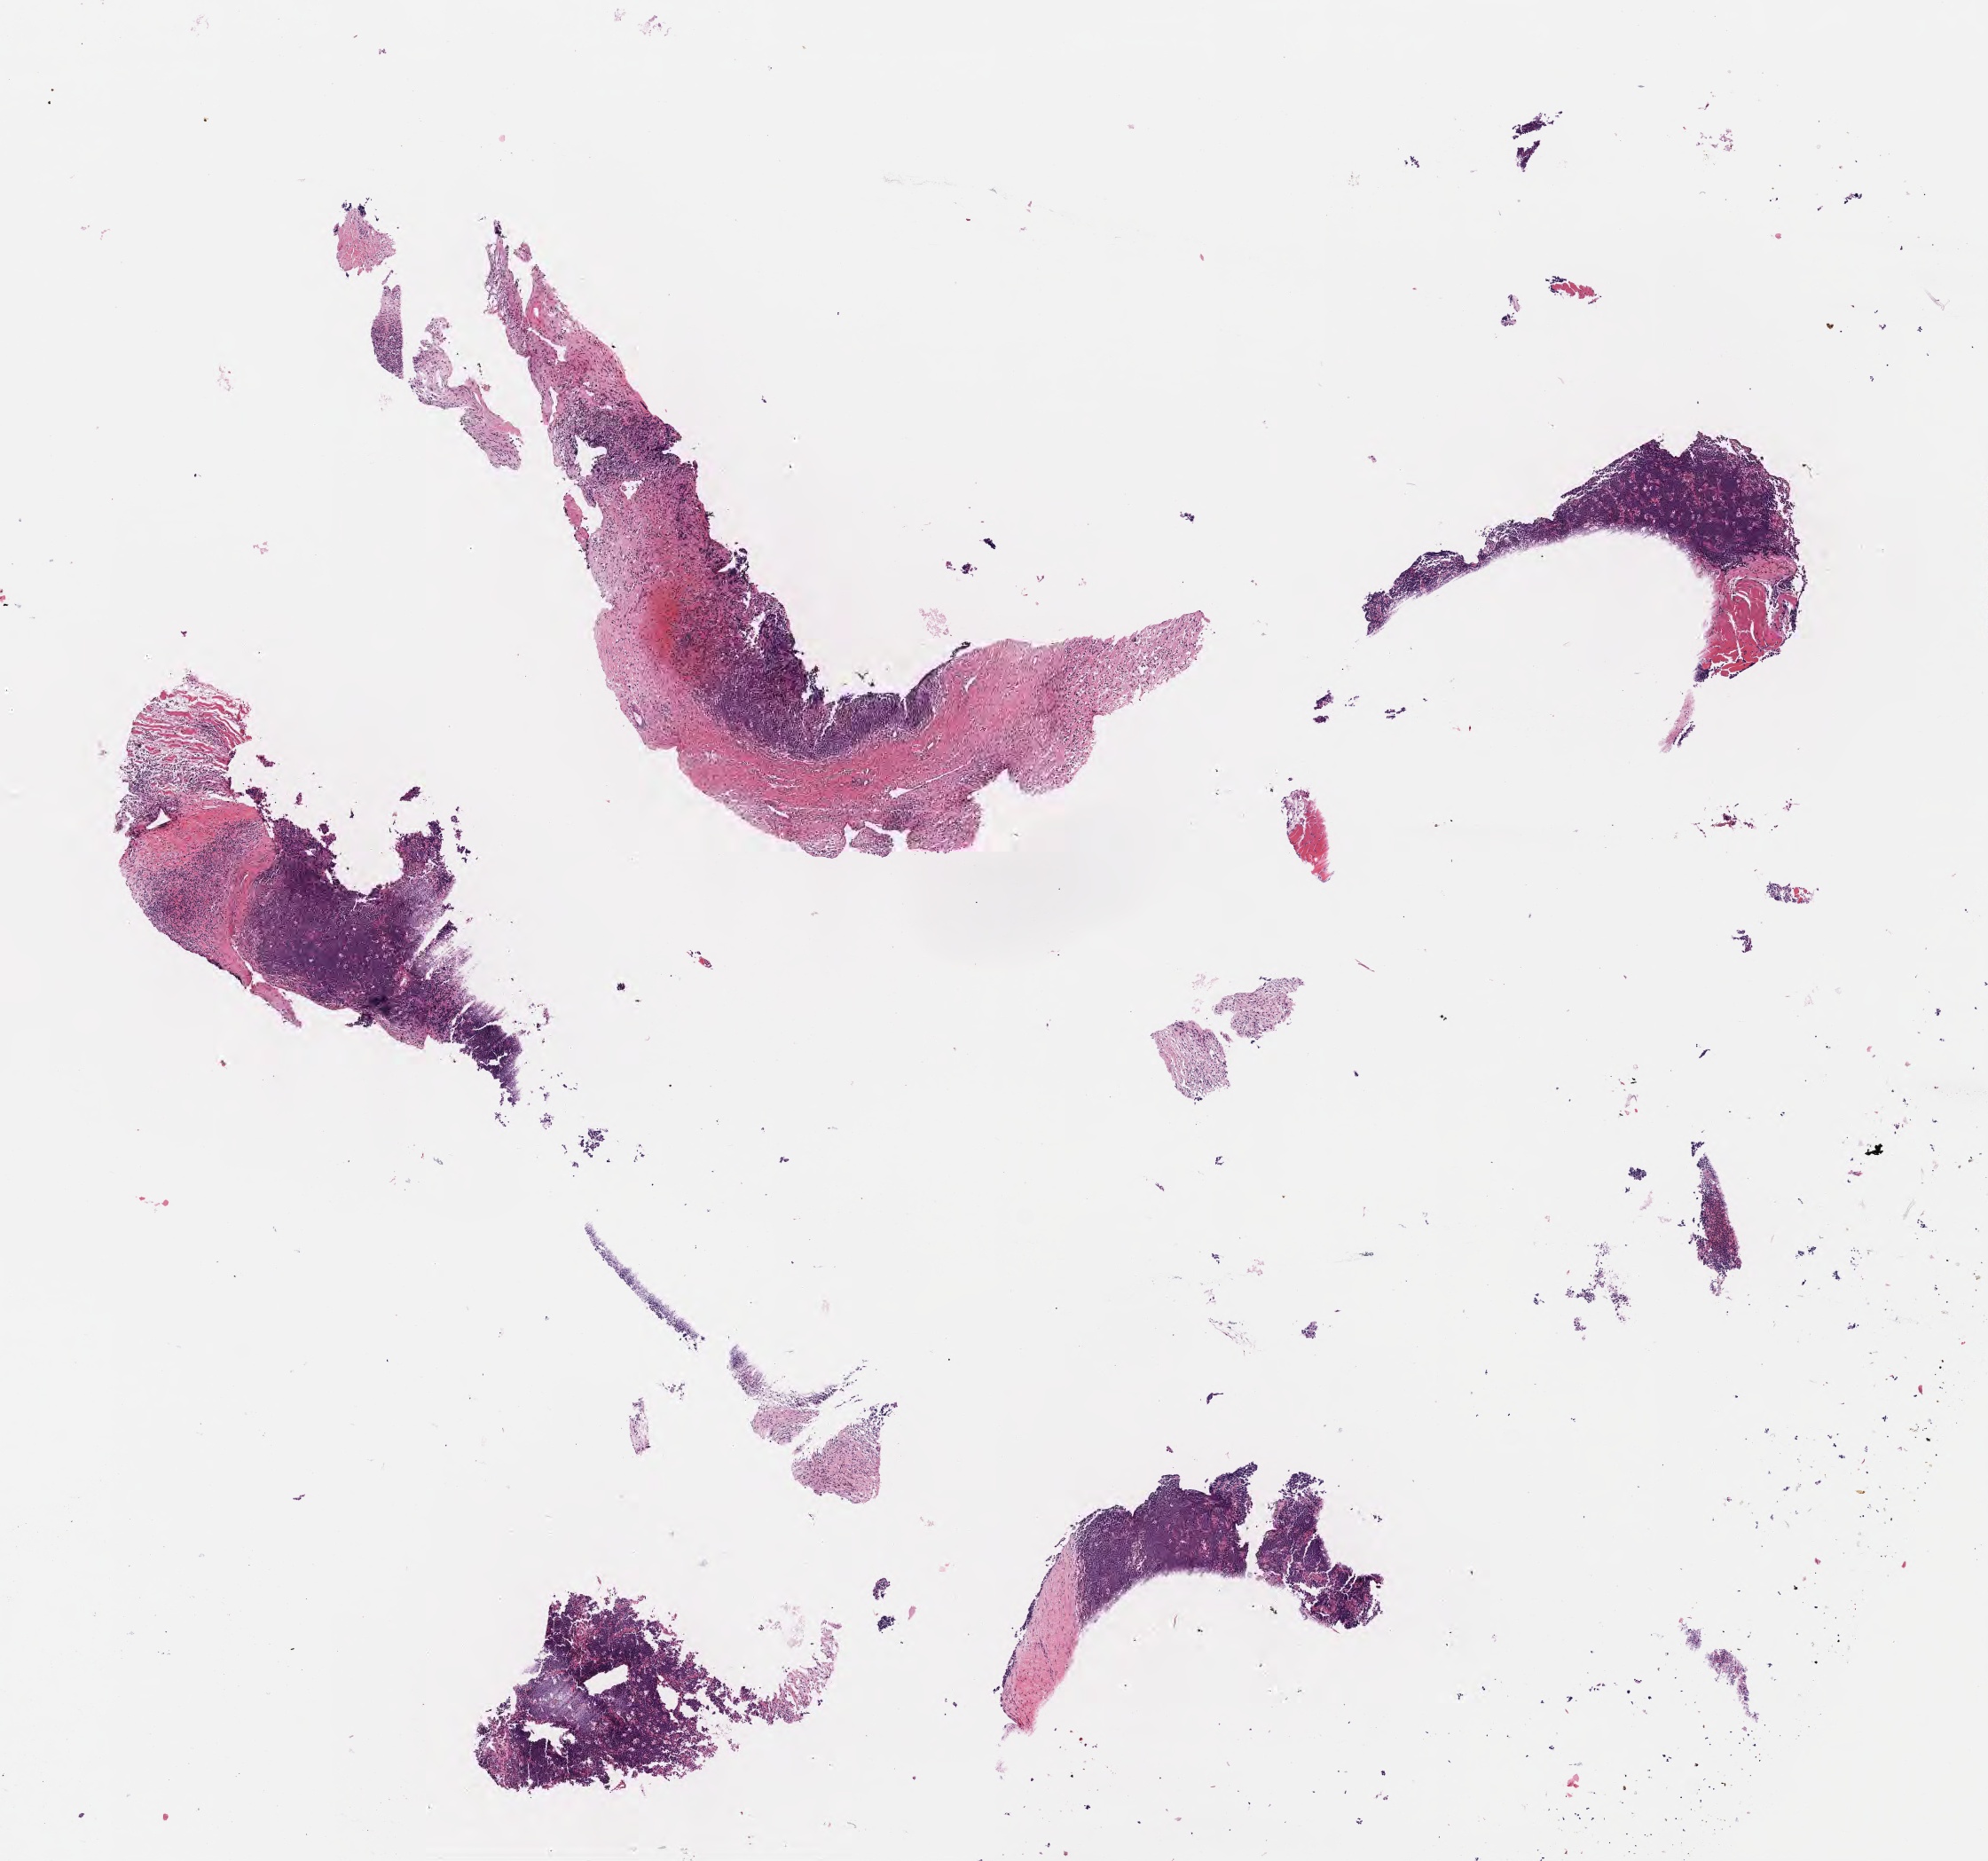
Whole-slide image, hematoxylin and eosin (H&E) stain, whole scanned area (about 9.1 x 8.5 mm) shown as a low-resolution overview. Specimen: tumor tissue. Female, age 9 years at initial diagnosis.
Diagnosis: Burkitt lymphoma, NOS.